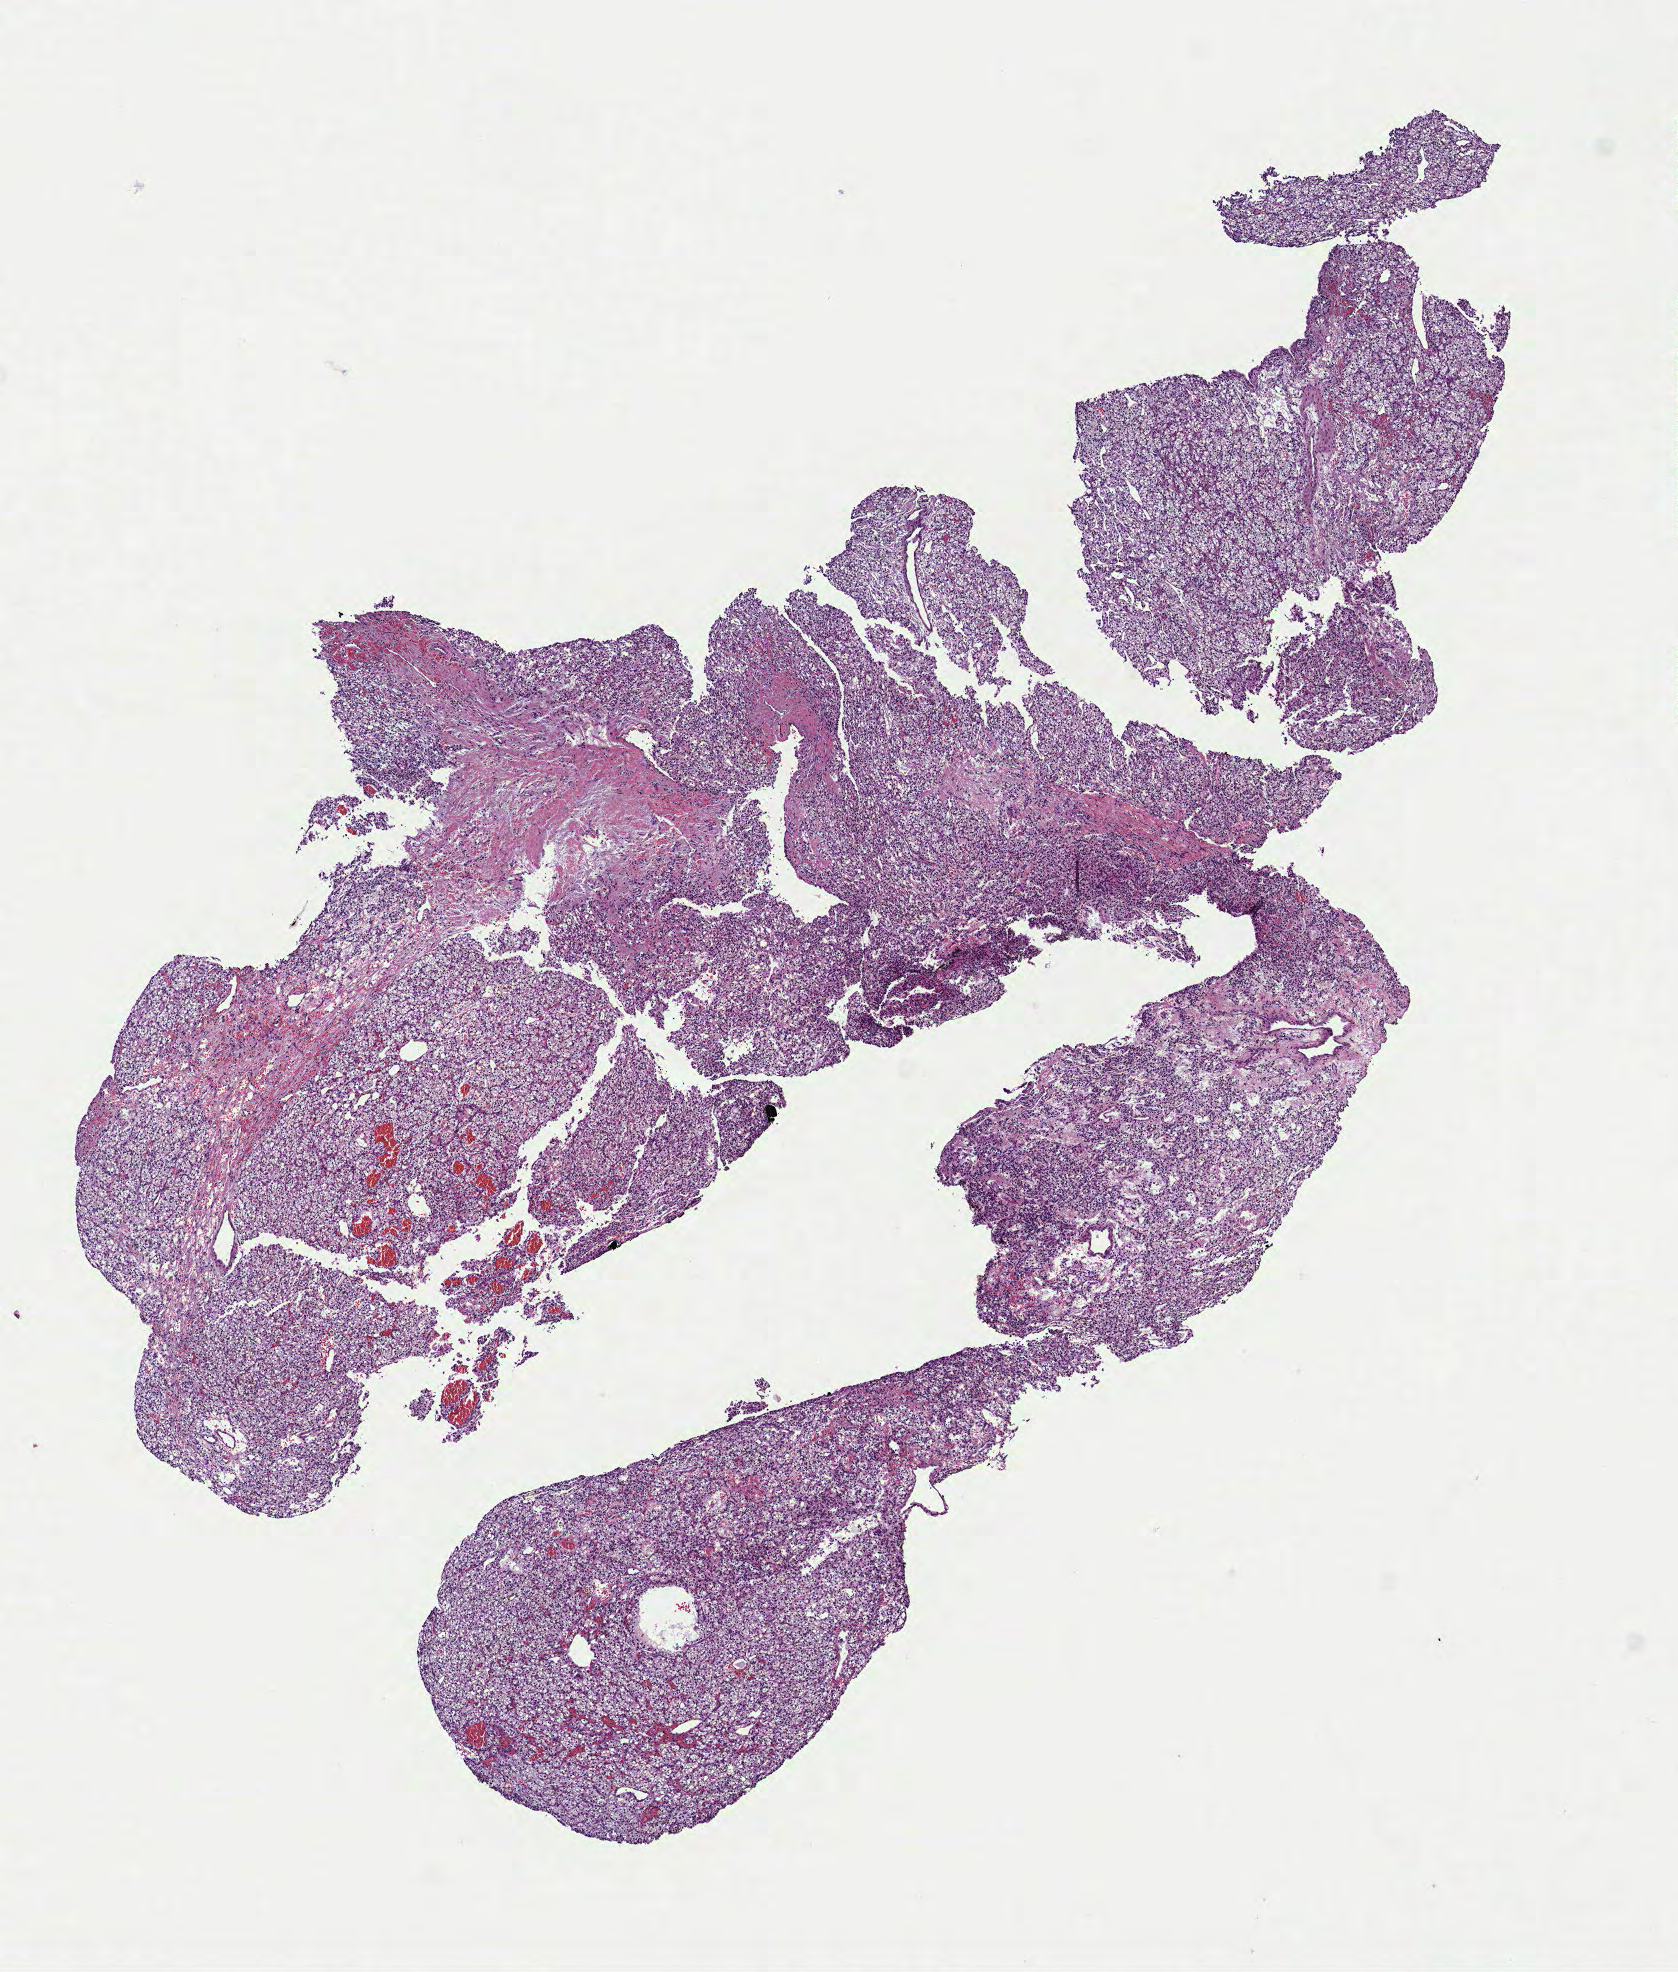
Hematoxylin and eosin (H&E) stained whole-slide image, low-resolution overview of the scanned area, about 6.8 x 8.0 mm (slide scanned at 40x), FFPE section, primary tumour sample from the kidney. Patient: female, age at initial diagnosis 59 years.
Diagnosis: Clear cell adenocarcinoma, NOS.